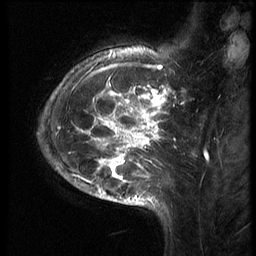
Breast MRI (dynamic contrast-enhanced), one sagittal slice; slice 18 of 70 in the series (ordered by position); 3 images stored at this slice position (order not interpretable as contrast timing); 1.5 T; TE 4.2 ms, TR 9 ms; 2.5 mm slice thickness; 256 × 256 image matrix, field of view 180 × 180 mm. Patient: female, 28 years. From the clinical record (not read from this slice): setting: breast cancer imaged before/during neoadjuvant chemotherapy.
Annotated regions visible in this slice (semi-automatic segmentation, software-assisted and operator-edited):
- analysis volume of interest (the breast-tissue region the enhancement analysis was run in; not a lesion): bounding box (x1, y1, x2, y2) in pixels: (43, 42, 186, 215)
- tumour enhancement mask (voxels above the 140 % enhancement threshold inside the analysis volume of interest): (62, 51, 172, 207)